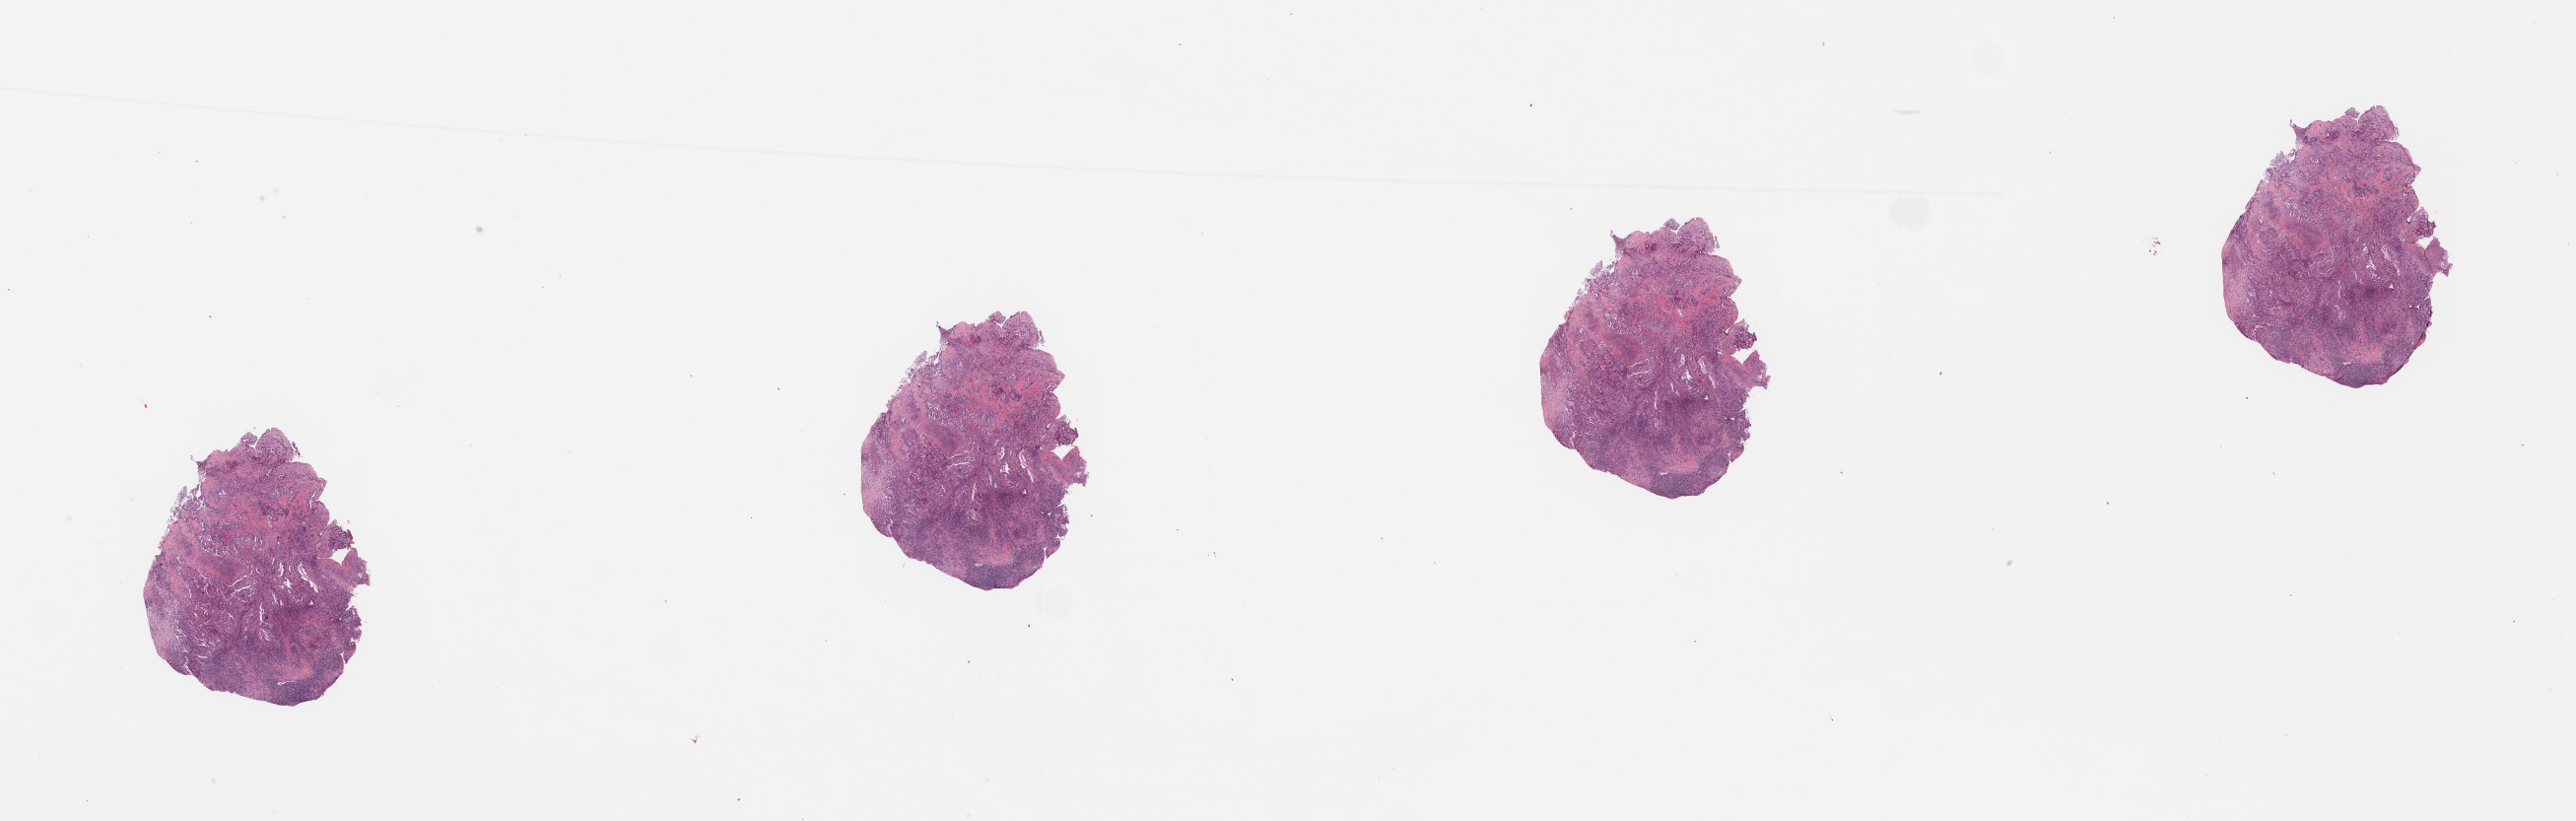
H&E whole-slide image, a low-resolution overview of the entire scanned area, about 41.3 x 13.2 mm; pancreas, tumour tissue. Female, 60 y/o. Histologic grade: G2 (moderately differentiated).
AJCC pathologic stage: IIB. Histologic diagnosis: Infiltrating duct carcinoma, NOS. Primary tumour site (as recorded): head.